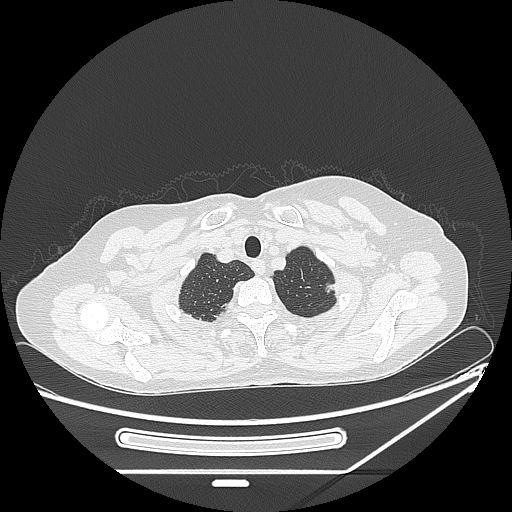
Chest CT, one axial slice. Position 217 of 250 along the scan axis. Reconstruction kernel LUNG. Lung window (W 1500 / L -600 HU). 1.25 mm slice thickness. 512 × 512 image matrix. Female patient, age 57 years. From the clinical record (not read from this slice): clinical TNM (as recorded): T1c N0 M0; histopathological grade: G2-3.
Structures marked on this image (rectangle marked by the reading radiologist):
- lung tumour (recorded histology: adenocarcinoma): bounding box (x1, y1, x2, y2) in pixels: (320, 280, 338, 295)